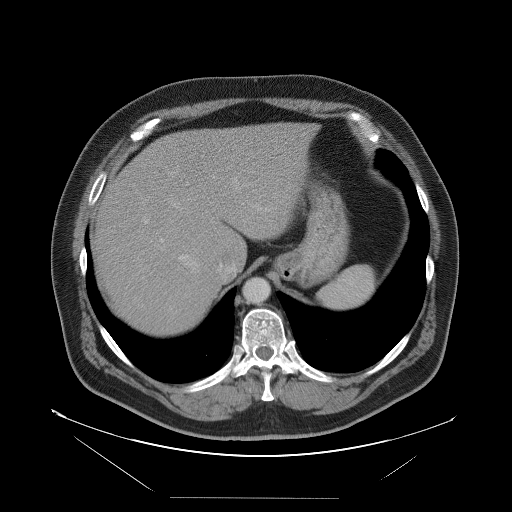
Contrast-enhanced abdominal CT, one axial slice; slice 78 of 114 in the series (ordered by position); soft-tissue window (W 400 / L 40 HU); 512 × 512 image matrix, field of view 500 × 500 mm. Male patient, age 61 years. From the clinical record (not read from this slice): diagnosis: colorectal cancer liver metastases, imaged before liver resection; multiple liver metastases: no; largest metastasis: 6.5 cm; disease in both lobes: yes.
Annotated regions visible in this slice (outlined manually by an expert reader):
- hepatic veins: box from (x=168, y=177) to (x=273, y=280) px
- liver: (x=91, y=124)–(x=315, y=337)
- planned liver remnant (the part of the liver to remain after resection): (x=147, y=124)–(x=314, y=266)
- portal vein (with intrahepatic branches): (x=144, y=219)–(x=164, y=242)